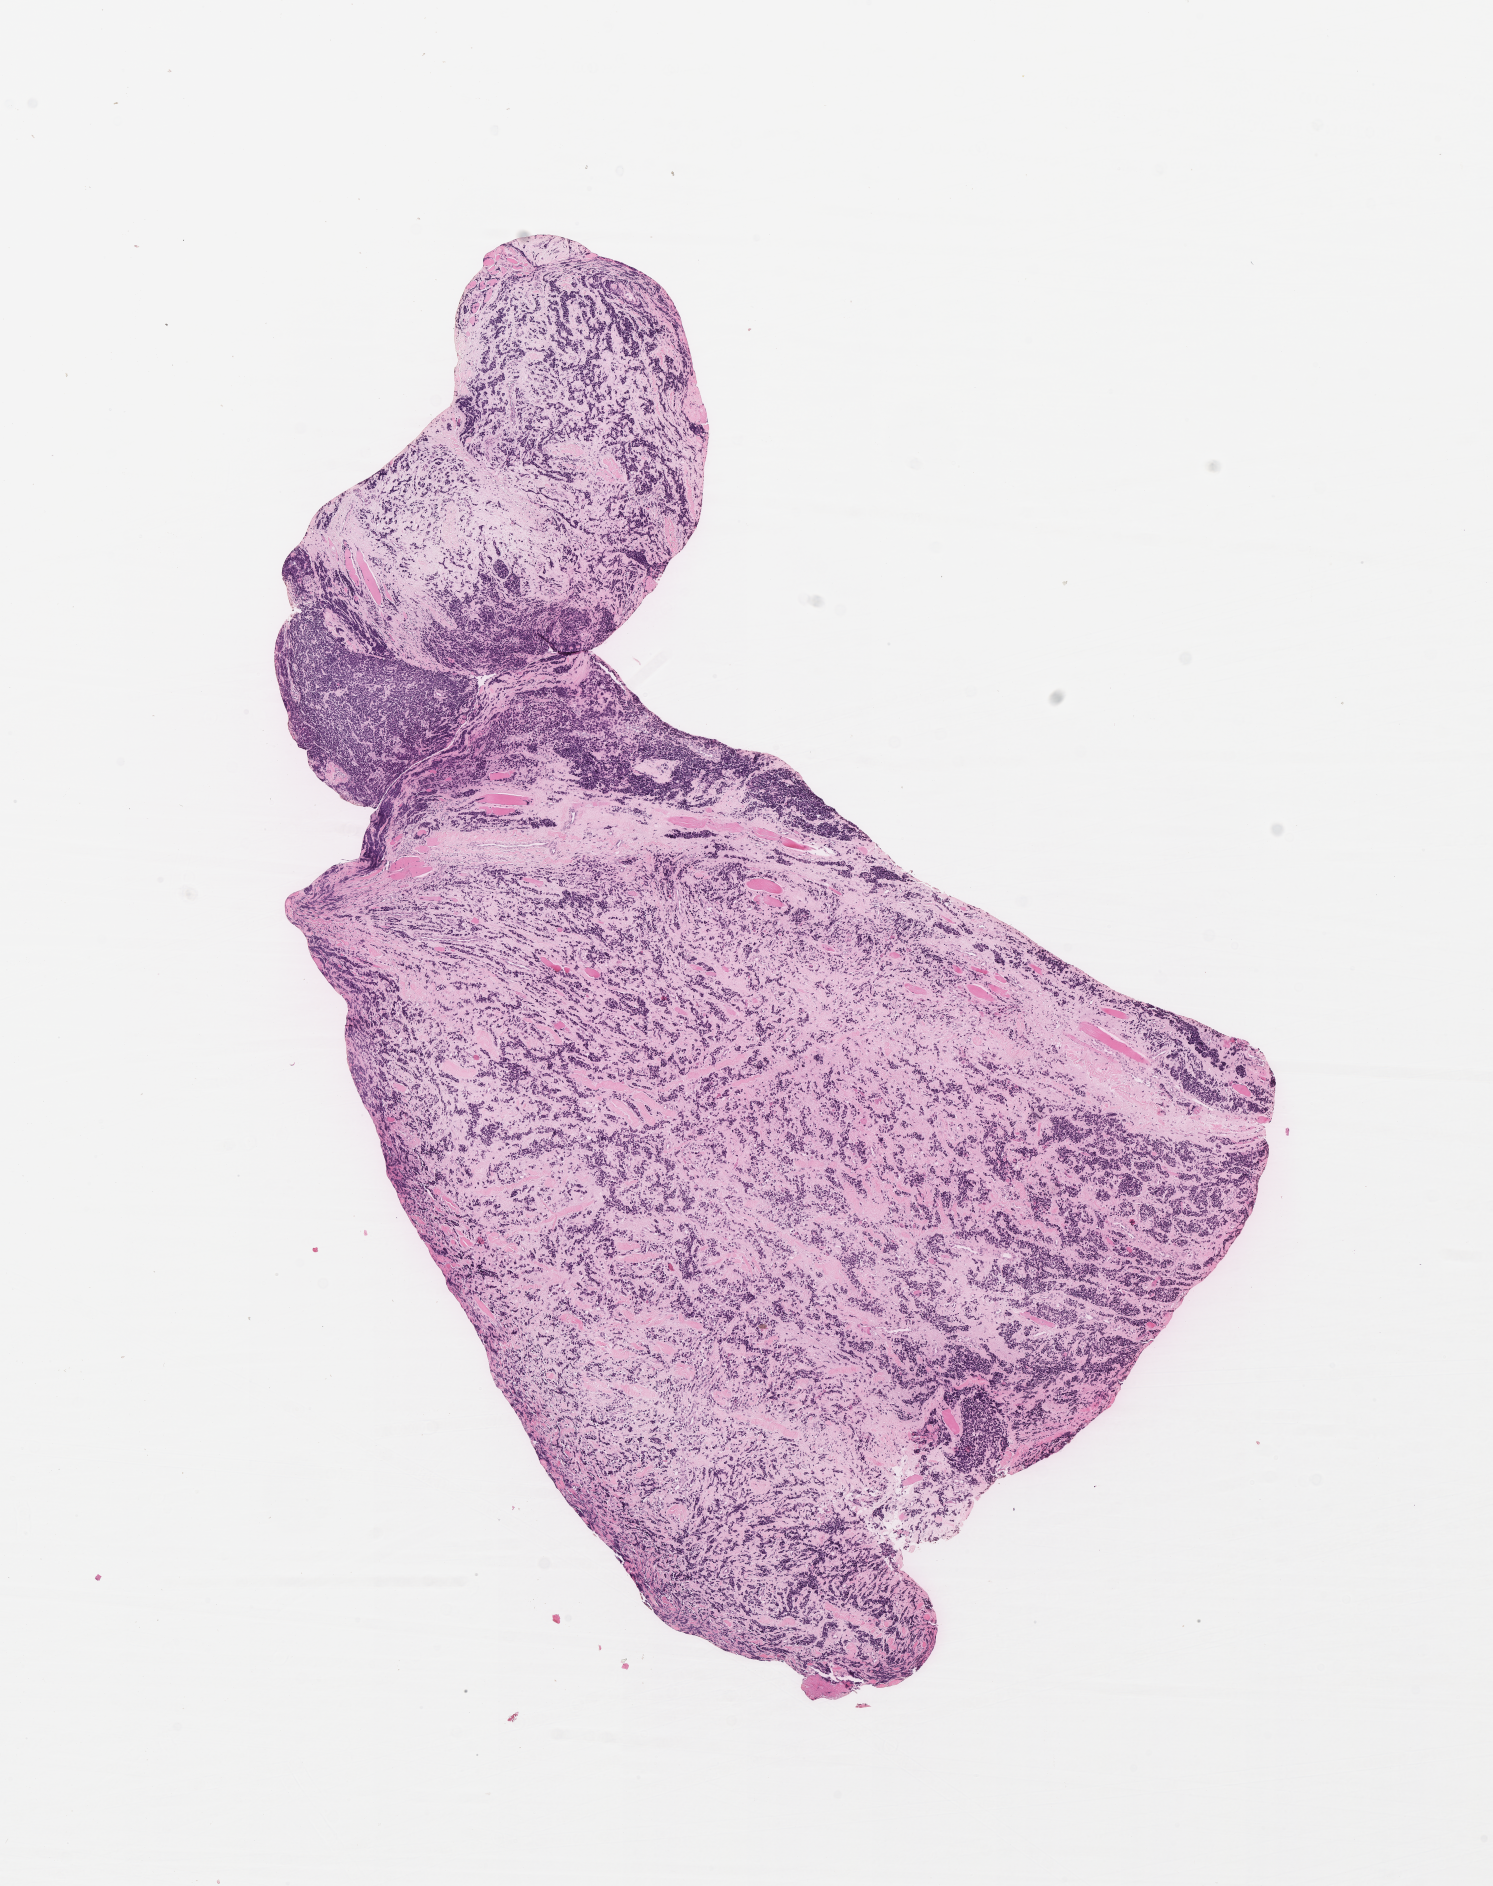
Hematoxylin and eosin (H&E) whole-slide image of tumor tissue — a low-resolution overview of the entire scanned area, about 6.0 x 7.6 mm, FFPE section, site: soft tissue, foot. Patient: male, age 15.2 years at diagnosis.
Metastatic status at presentation (as recorded): metastatic (confirmed). Stage (as recorded): 4. Diagnosis: rhabdomyosarcoma; histological classification: alveolar rhabdomyosarcoma.